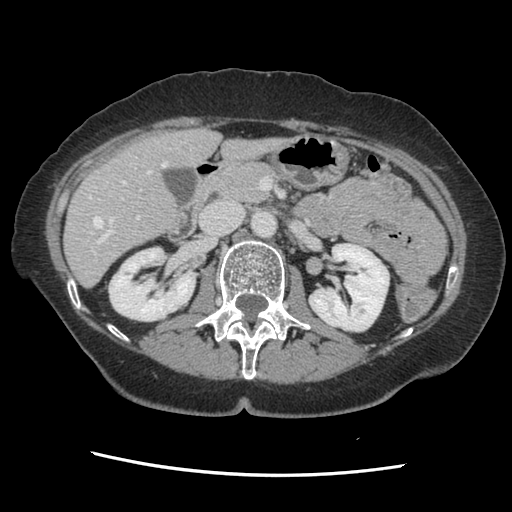
Contrast-enhanced abdominal CT, one axial slice. Position 68 of 141 along the scan axis. 120 kVp. Soft-tissue window (W 400 / L 40 HU). 2.5 mm slice thickness. 512 × 512 image matrix, field of view 330 × 330 mm. Female patient, age 61 years. Case-level facts recorded for this patient, not image findings: diagnosis: colorectal cancer liver metastases, imaged before liver resection; multiple liver metastases: no; largest metastasis: 2.4 cm; disease in both lobes: no.
Structures marked on this image (manually delineated by an expert):
- hepatic veins: bounding box (x1, y1, x2, y2) in pixels: (89, 162, 167, 252)
- liver: (65, 129, 283, 285)
- planned liver remnant (the part of the liver to remain after resection): (65, 129, 283, 285)
- portal vein (with intrahepatic branches): (91, 181, 142, 251)